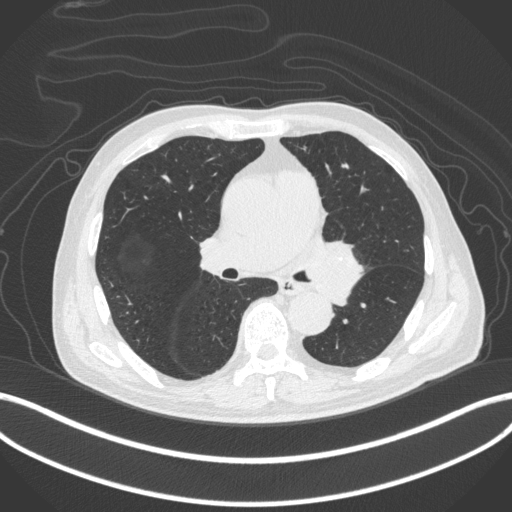
Chest CT, one axial slice; slice 244 of 420 in the series (ordered by position); 120 kVp; lung window (W 1500 / L -600 HU); 1 mm slice thickness; 512 × 512 image matrix, field of view 400 × 400 mm. Male patient, age 77 years. Case-level facts recorded for this patient, not image findings: clinical TNM (as recorded): T3 N1 M0.
Annotated regions visible in this slice (rectangle marked by the reading radiologist):
- lung tumour (recorded histology: adenocarcinoma): bounding box [x1, y1, x2, y2] px = [306, 240, 372, 309]